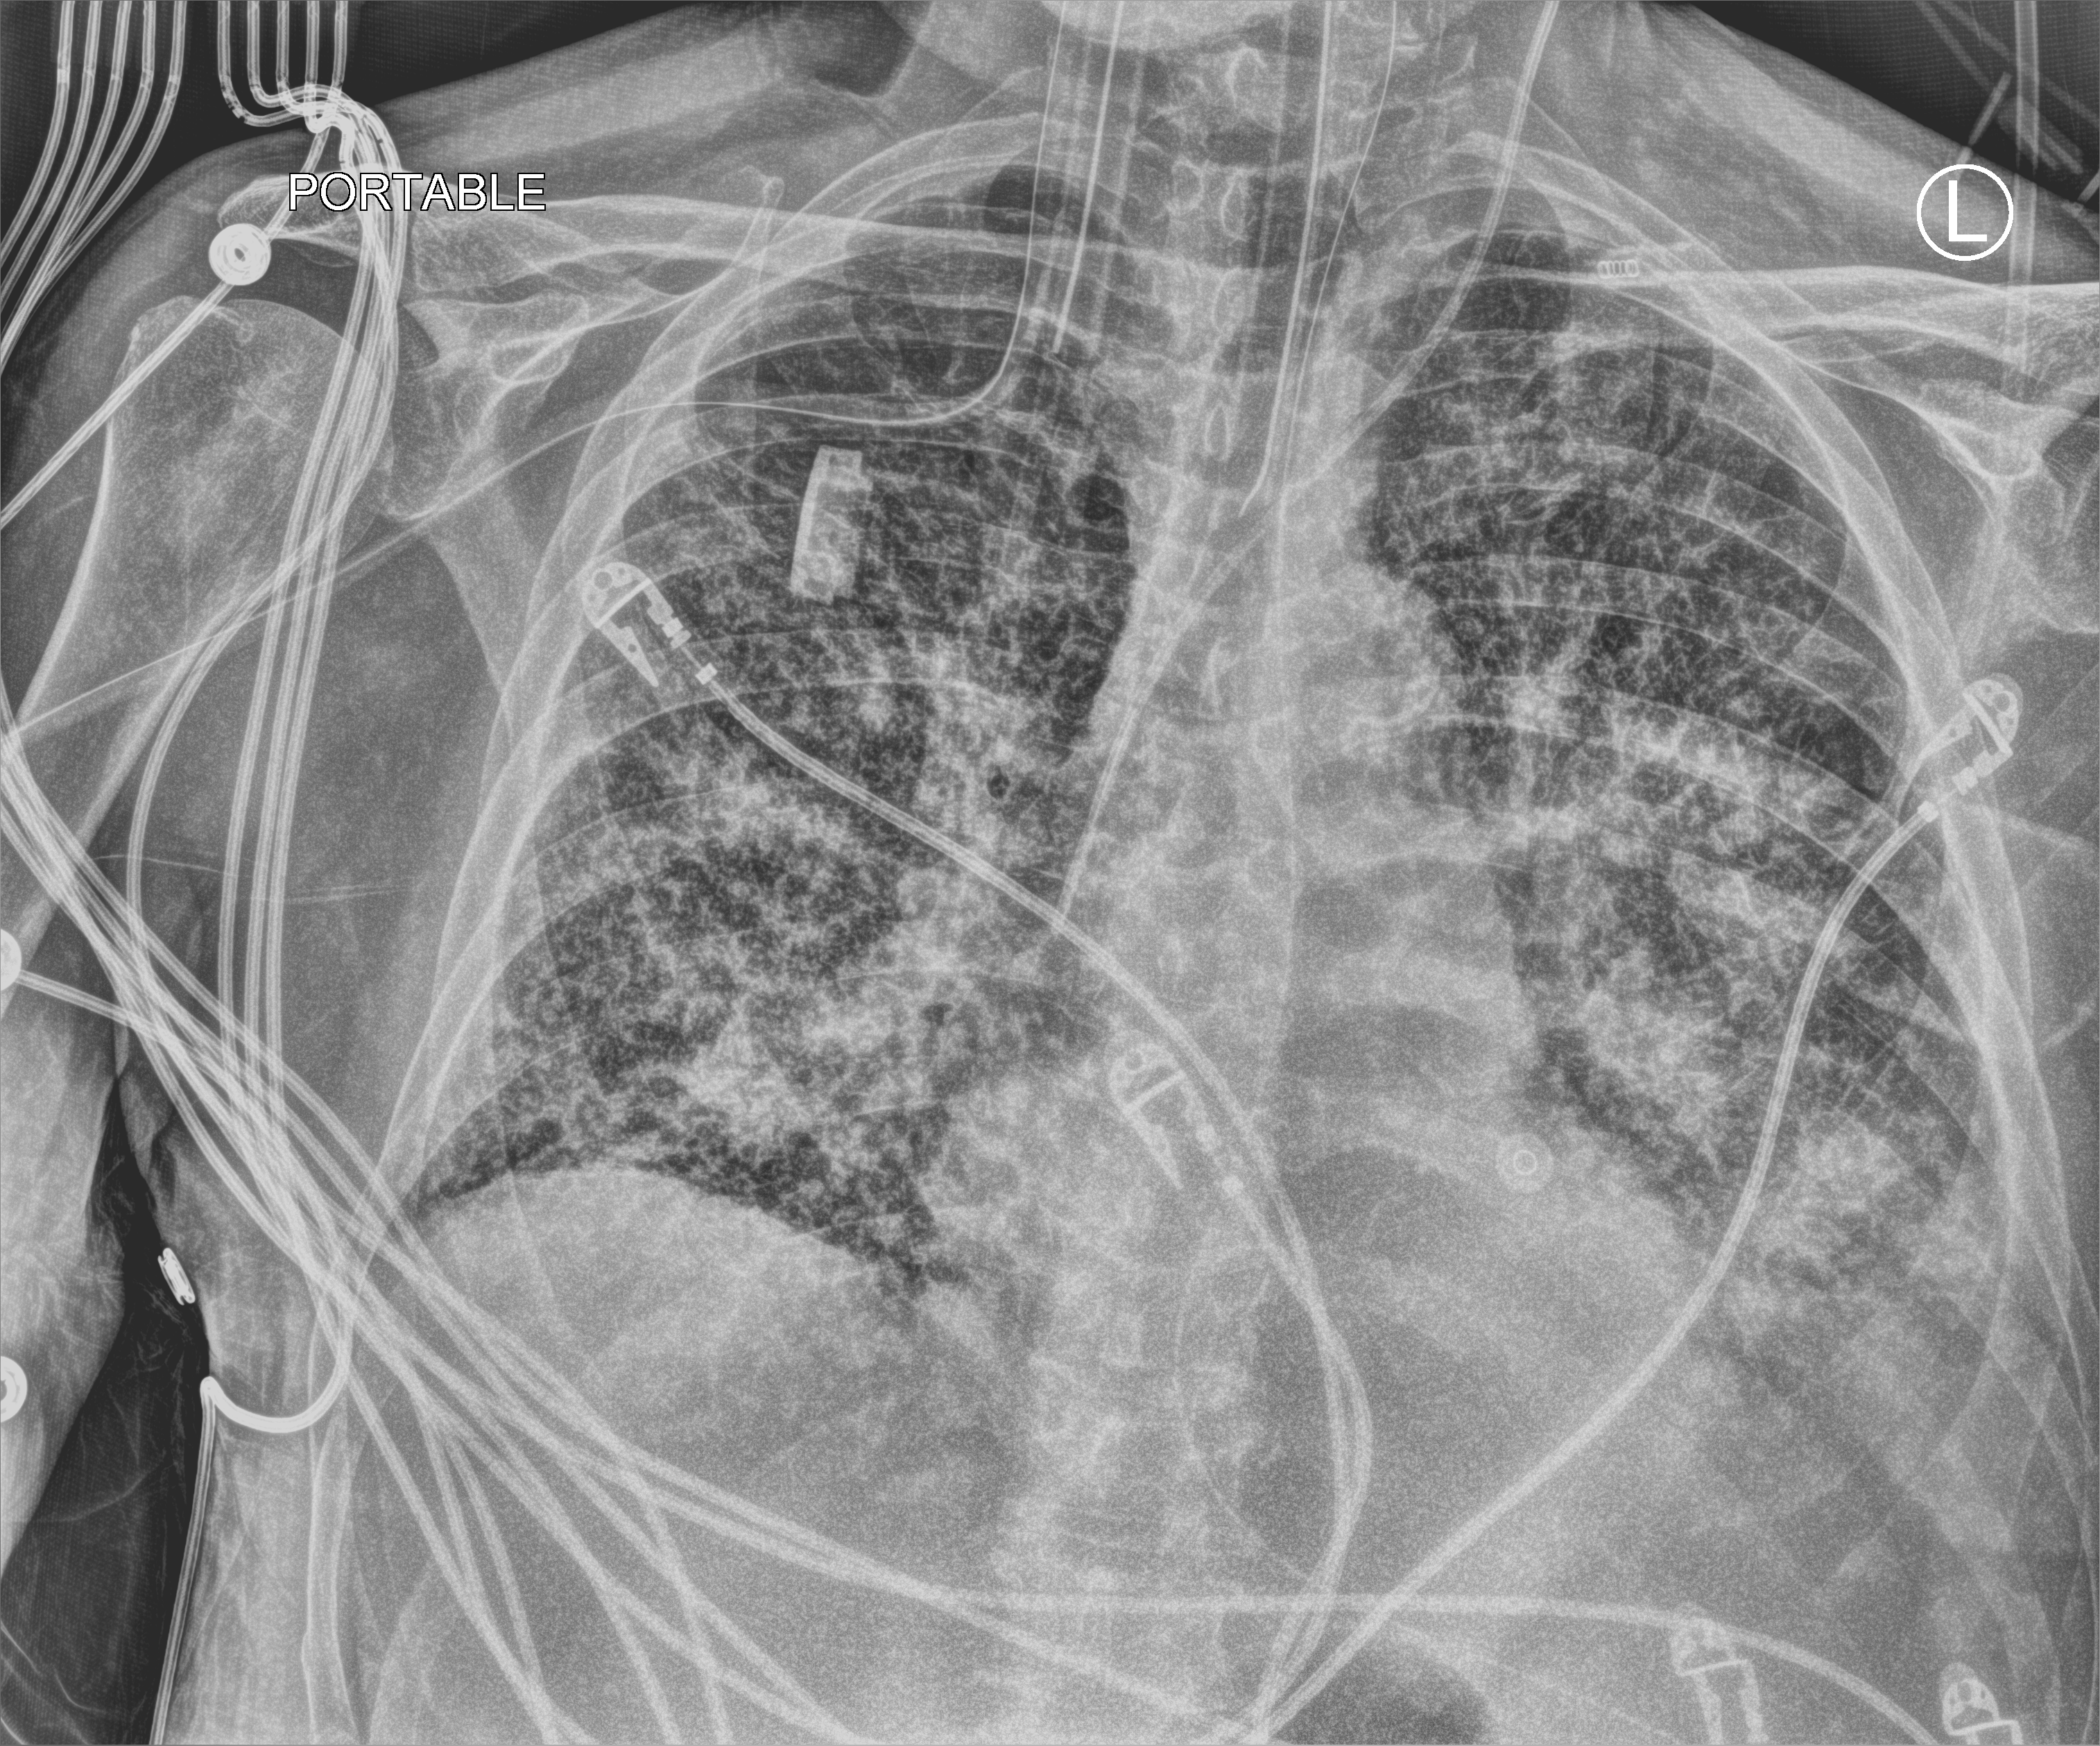
Chest X-ray (portable), anteroposterior (AP) projection. Patient hospitalised with COVID-19; male, aged 75–90 years.
Hospital-stay facts (about this admission, not read from this image; timing relative to this image not recorded):
- admitted to intensive care during this hospital stay: yes